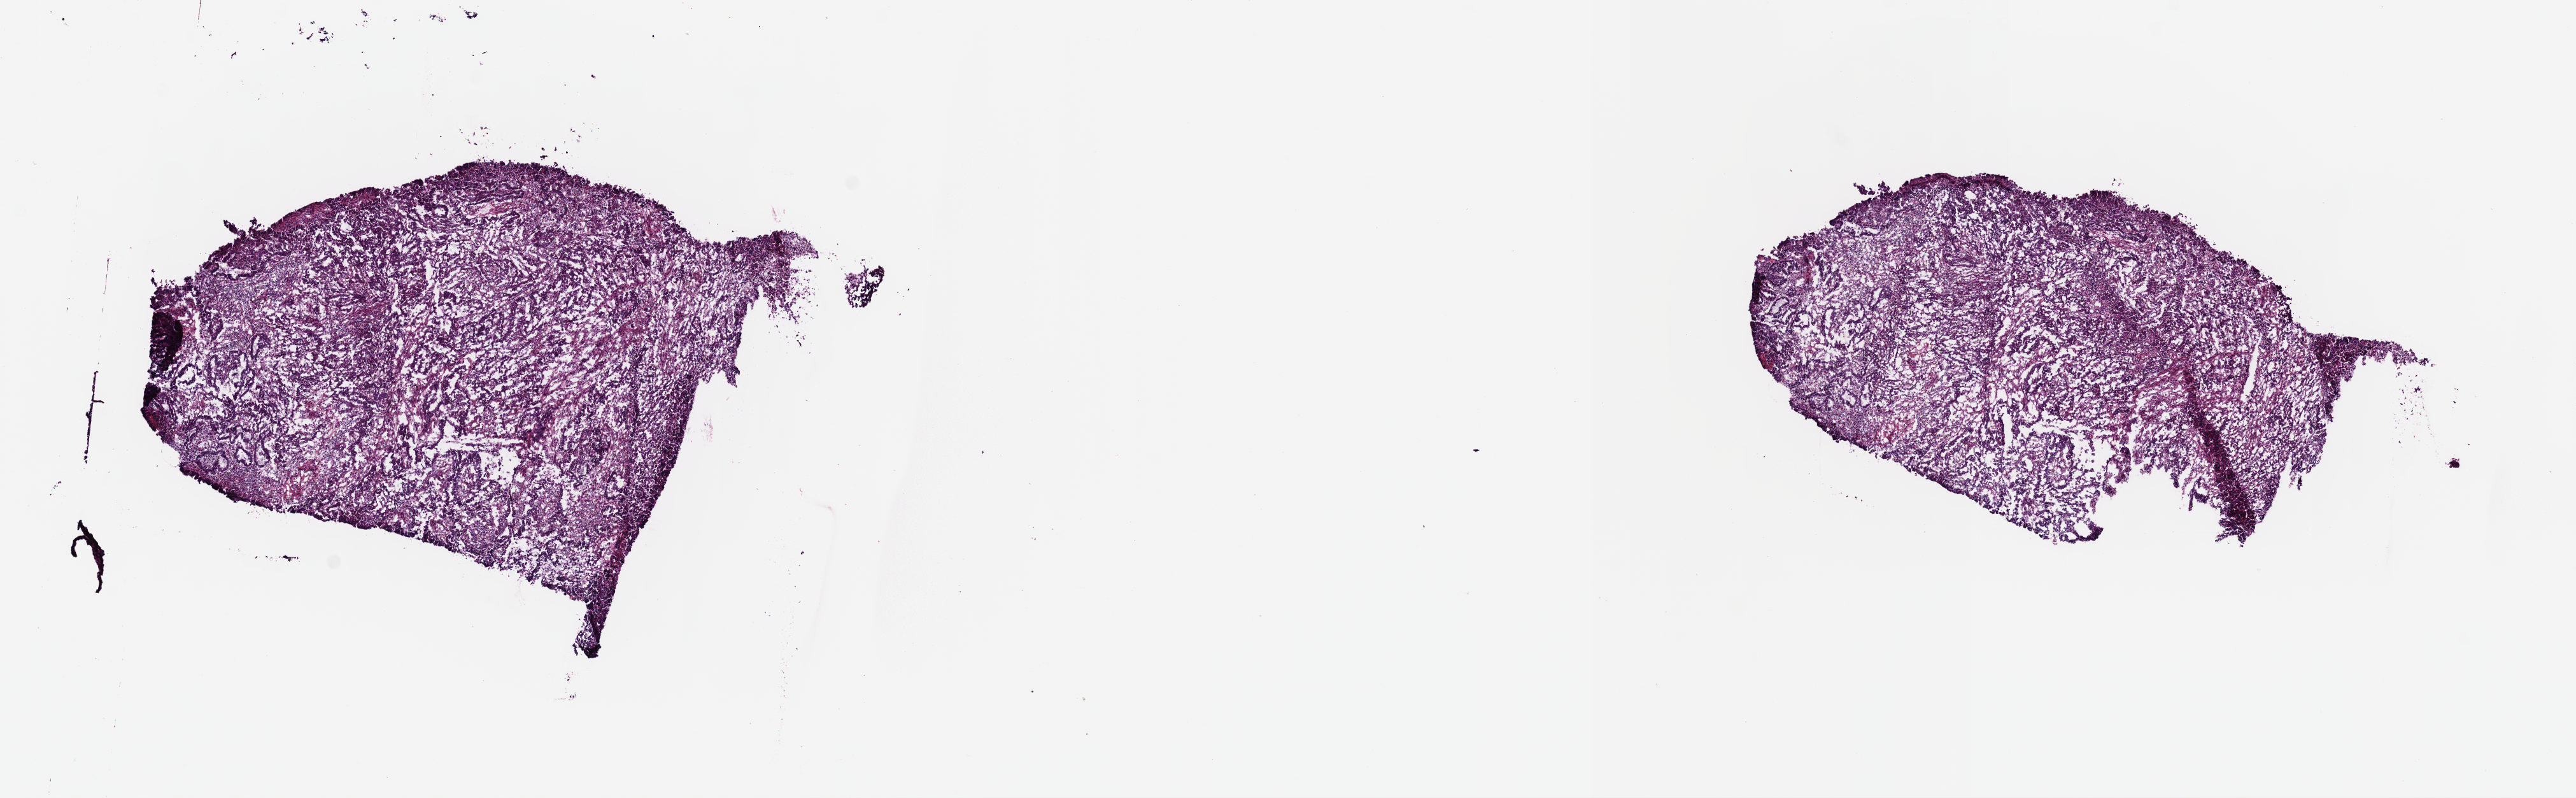
Digitized Hematoxylin and eosin (H&E) stained tissue section (whole slide), low-resolution overview of the scanned area, about 16.0 x 4.9 mm; frozen section from the top of the tissue portion; sample: primary tumour, uterus. Female, age 63 years at initial diagnosis. Histologic grade: G3 (poorly differentiated). Slide review estimates, as recorded: tumour cells 90%, tumour nuclei 90%, normal cells 0%, stromal cells 10%, necrosis 0%. Inflammatory infiltration, as recorded: lymphocyte infiltration 60%, monocyte infiltration 20%, neutrophil infiltration 20%.
Histologic diagnosis: Serous cystadenocarcinoma, NOS (endometrium). FIGO stage: IB.